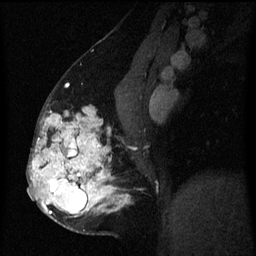
Breast MRI (dynamic contrast-enhanced), one sagittal slice. Slice 30 of 60 in the series (ordered by position). Dynamic contrast-enhanced series, image 2 of 3 at this slice position (ordered by acquisition). 1.5 T. TE 4.2 ms, TR 8 ms. 2 mm slice thickness. 256 × 256 image matrix. Female patient, age 50 years.
Outlined on this slice (semi-automatically segmented with operator editing):
- analysis volume of interest (the breast-tissue region the enhancement analysis was run in; not a lesion): bounding box (x1, y1, x2, y2) in pixels: (32, 108, 128, 232)
- tumour enhancement mask (voxels above the 70 % enhancement threshold inside the analysis volume of interest): (32, 108, 128, 217)